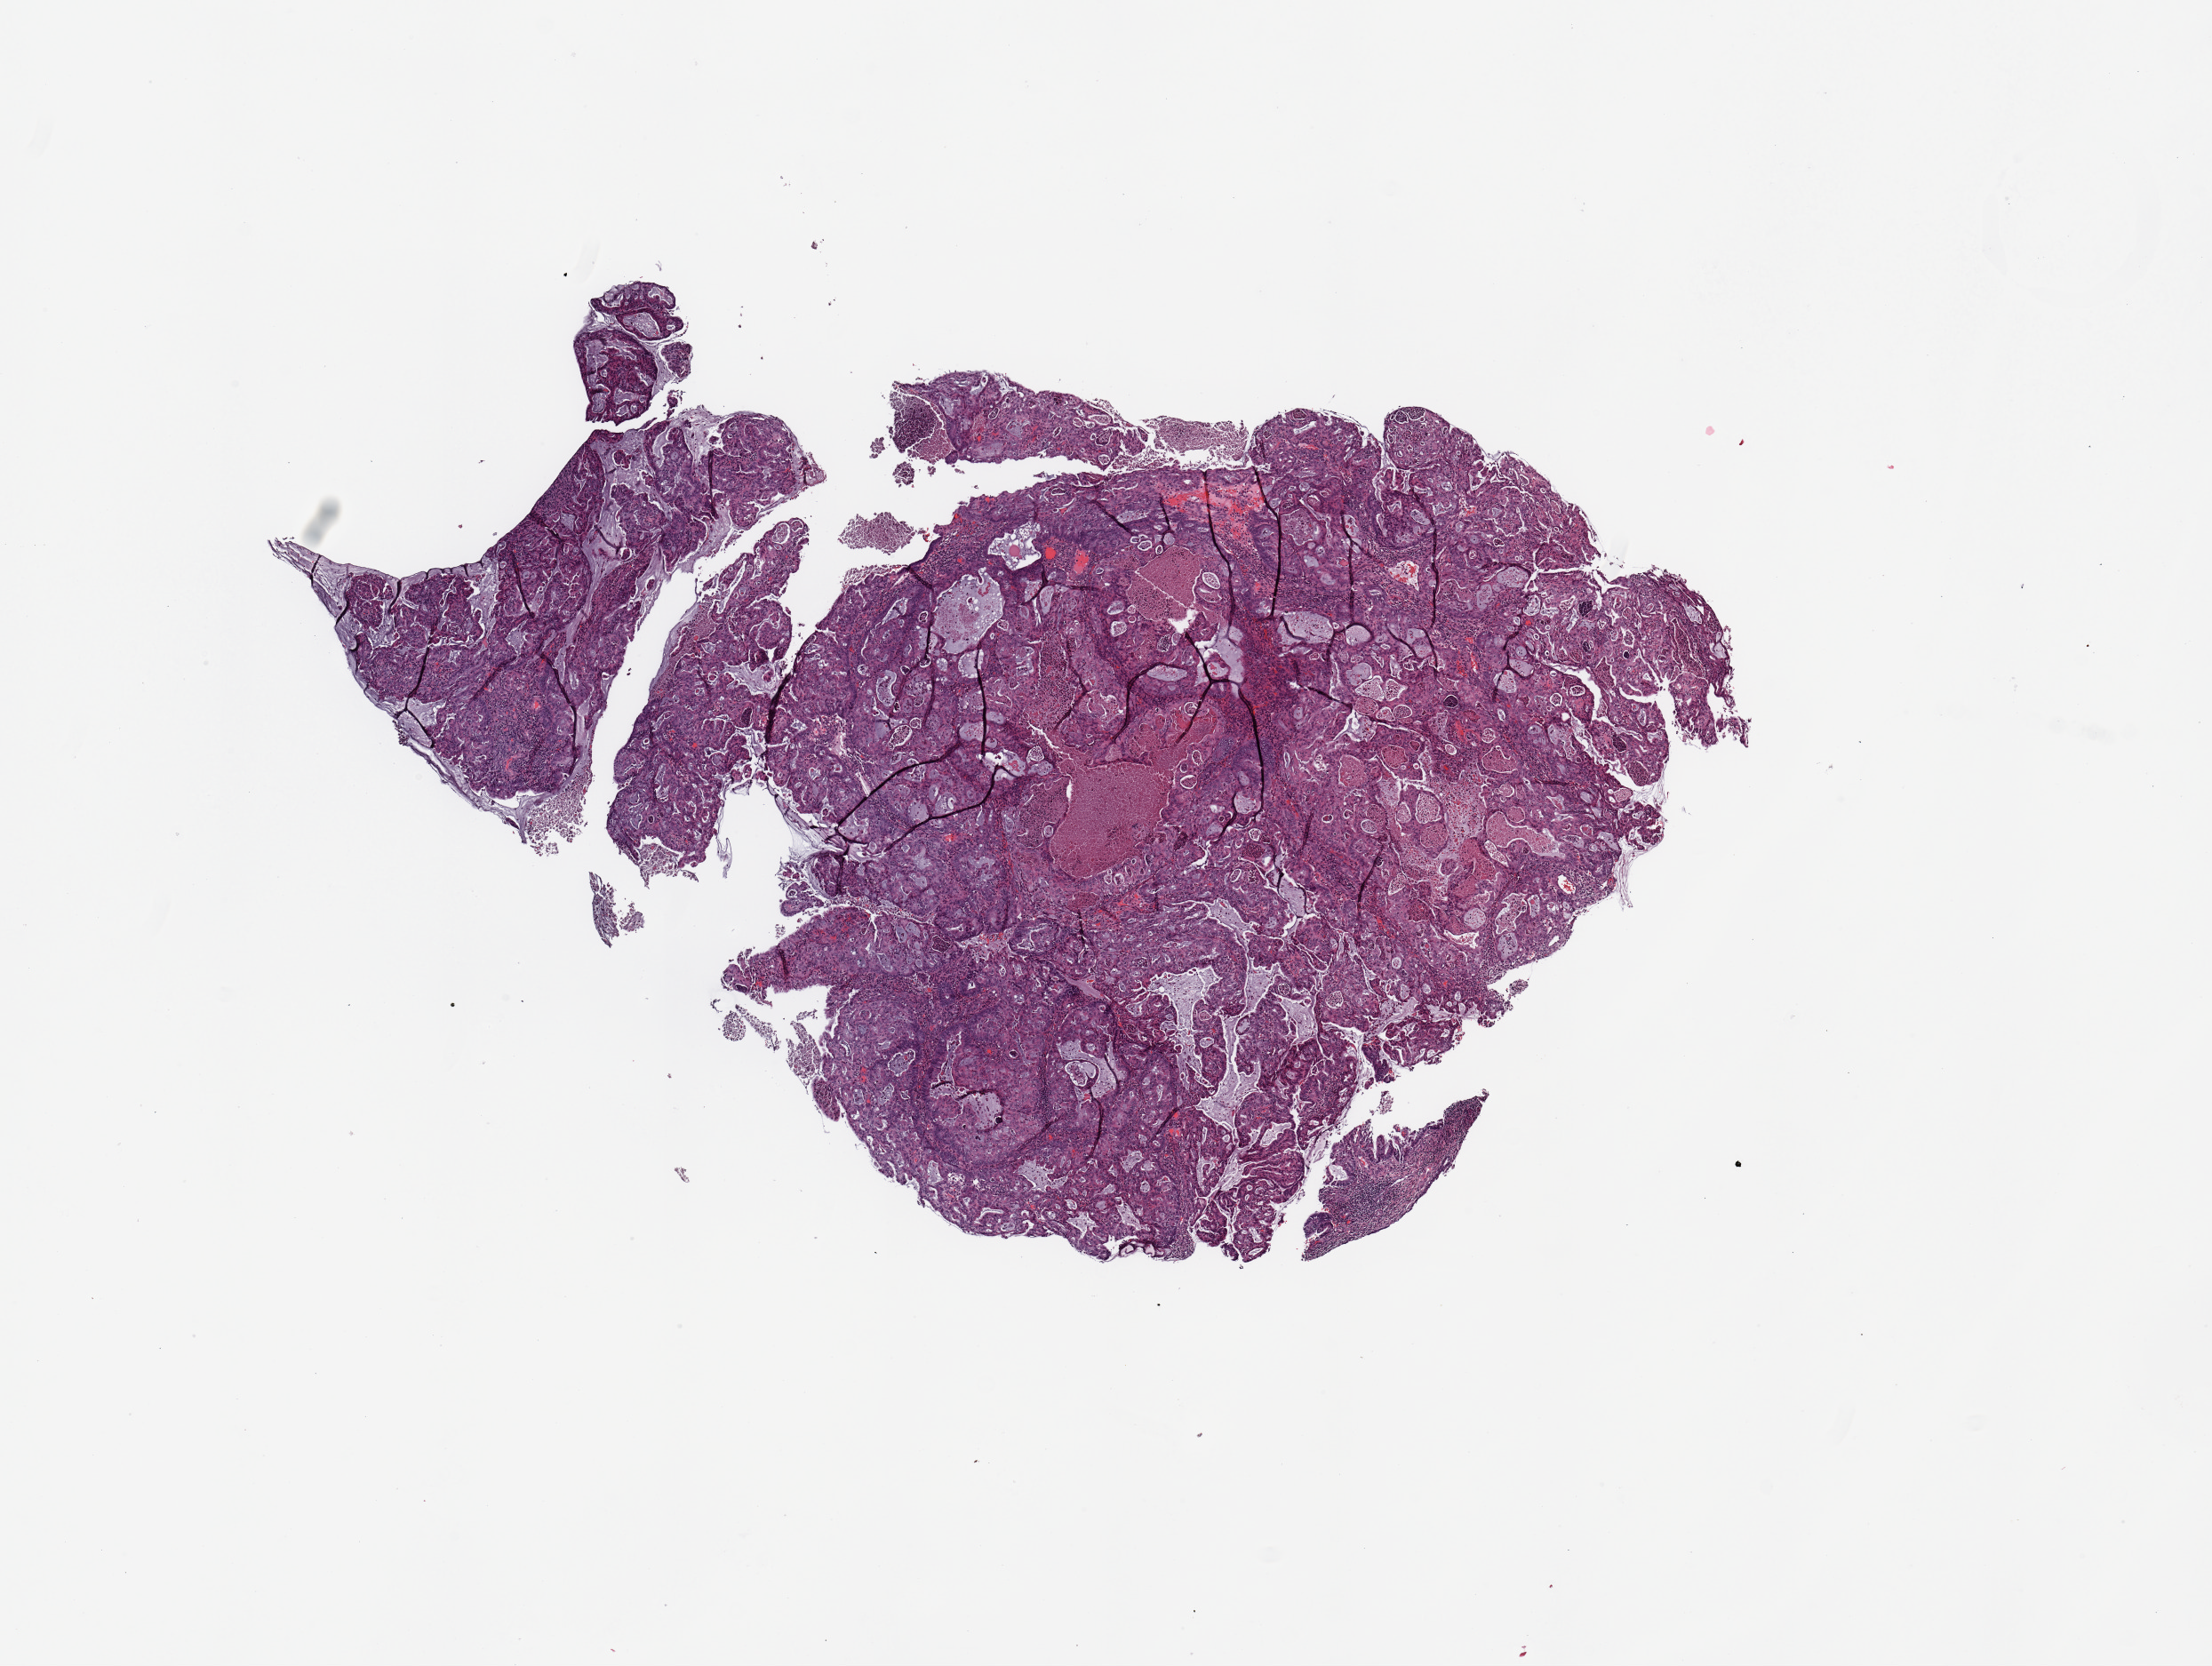
Whole-slide histology image, H&E, shown as a low-resolution overview of the whole scanned area (about 9.8 x 7.4 mm), tumour tissue sample, uterus. Female, 69 y/o. Histologic grade: G2 (moderately differentiated).
Diagnosis: Endometrioid adenocarcinoma, NOS. AJCC pathologic stage: IA.